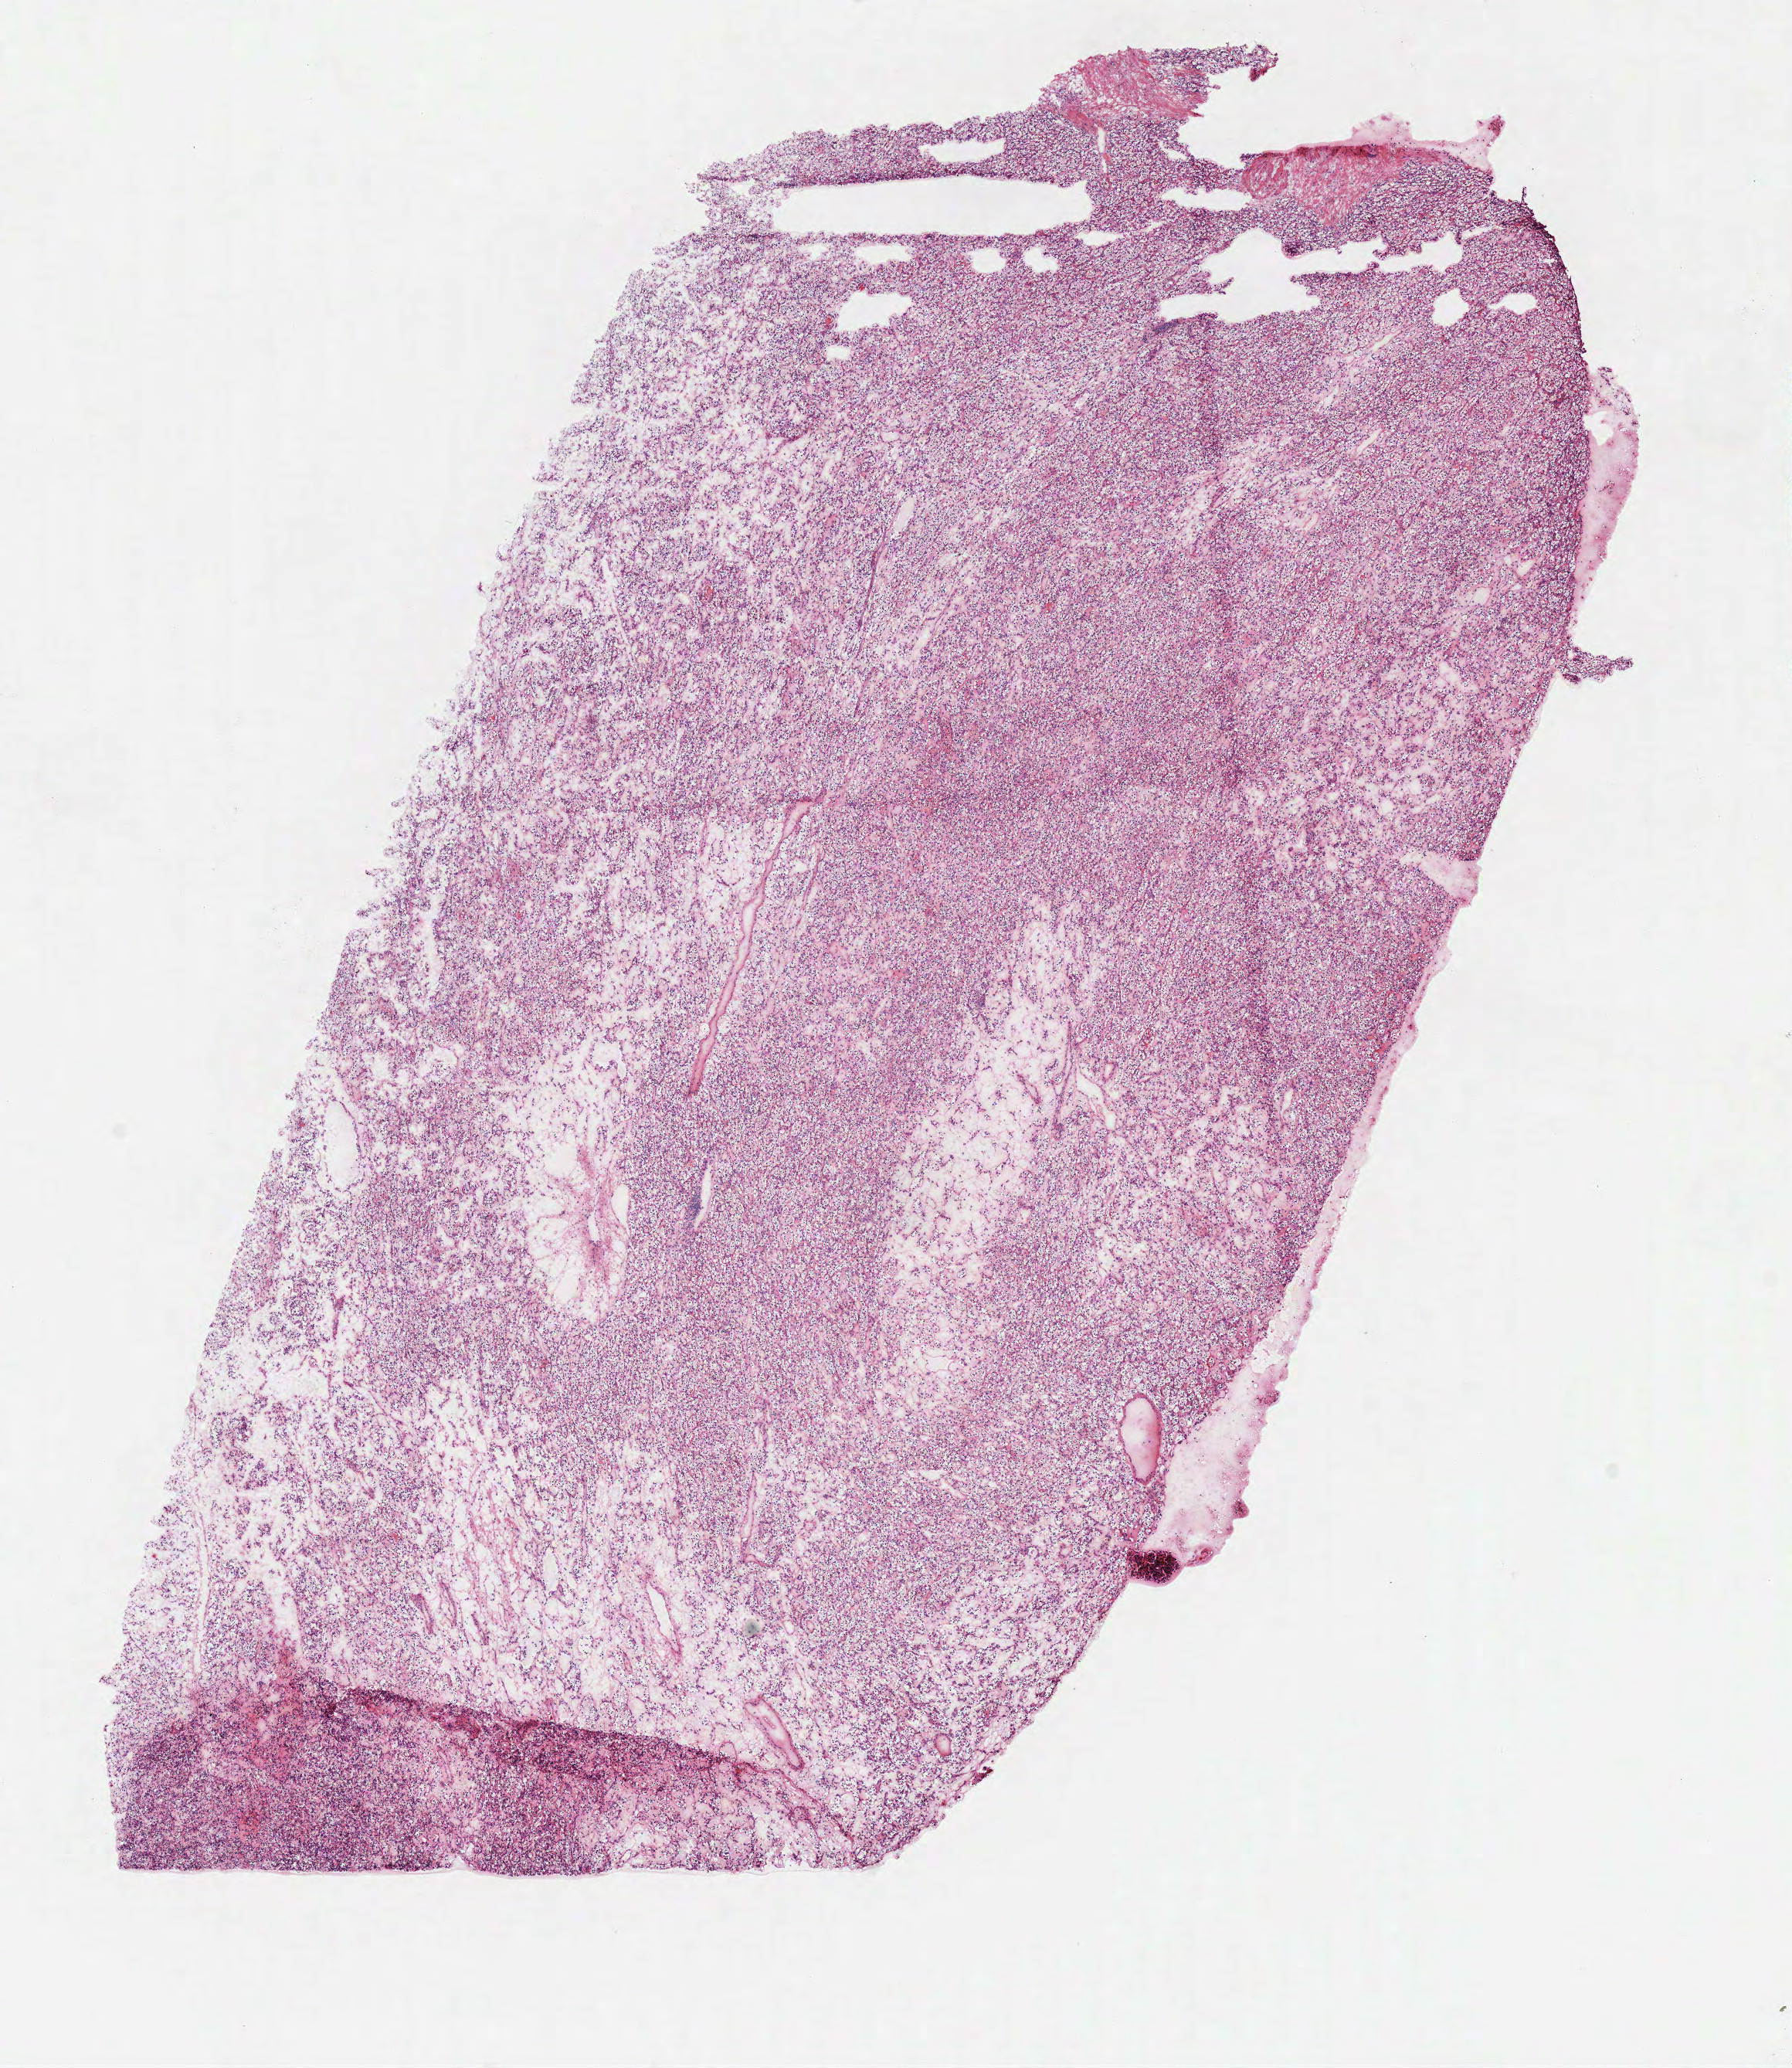
Whole-slide histology image, H&E-stained, whole scanned area (about 9.1 x 10.5 mm, slide scanned at 40x) shown as a low-resolution overview, frozen section from the top of the tissue portion, sample: primary tumour, kidney. Patient: male, age at initial diagnosis 73 years.
Pathologic diagnosis: Clear cell adenocarcinoma, NOS.